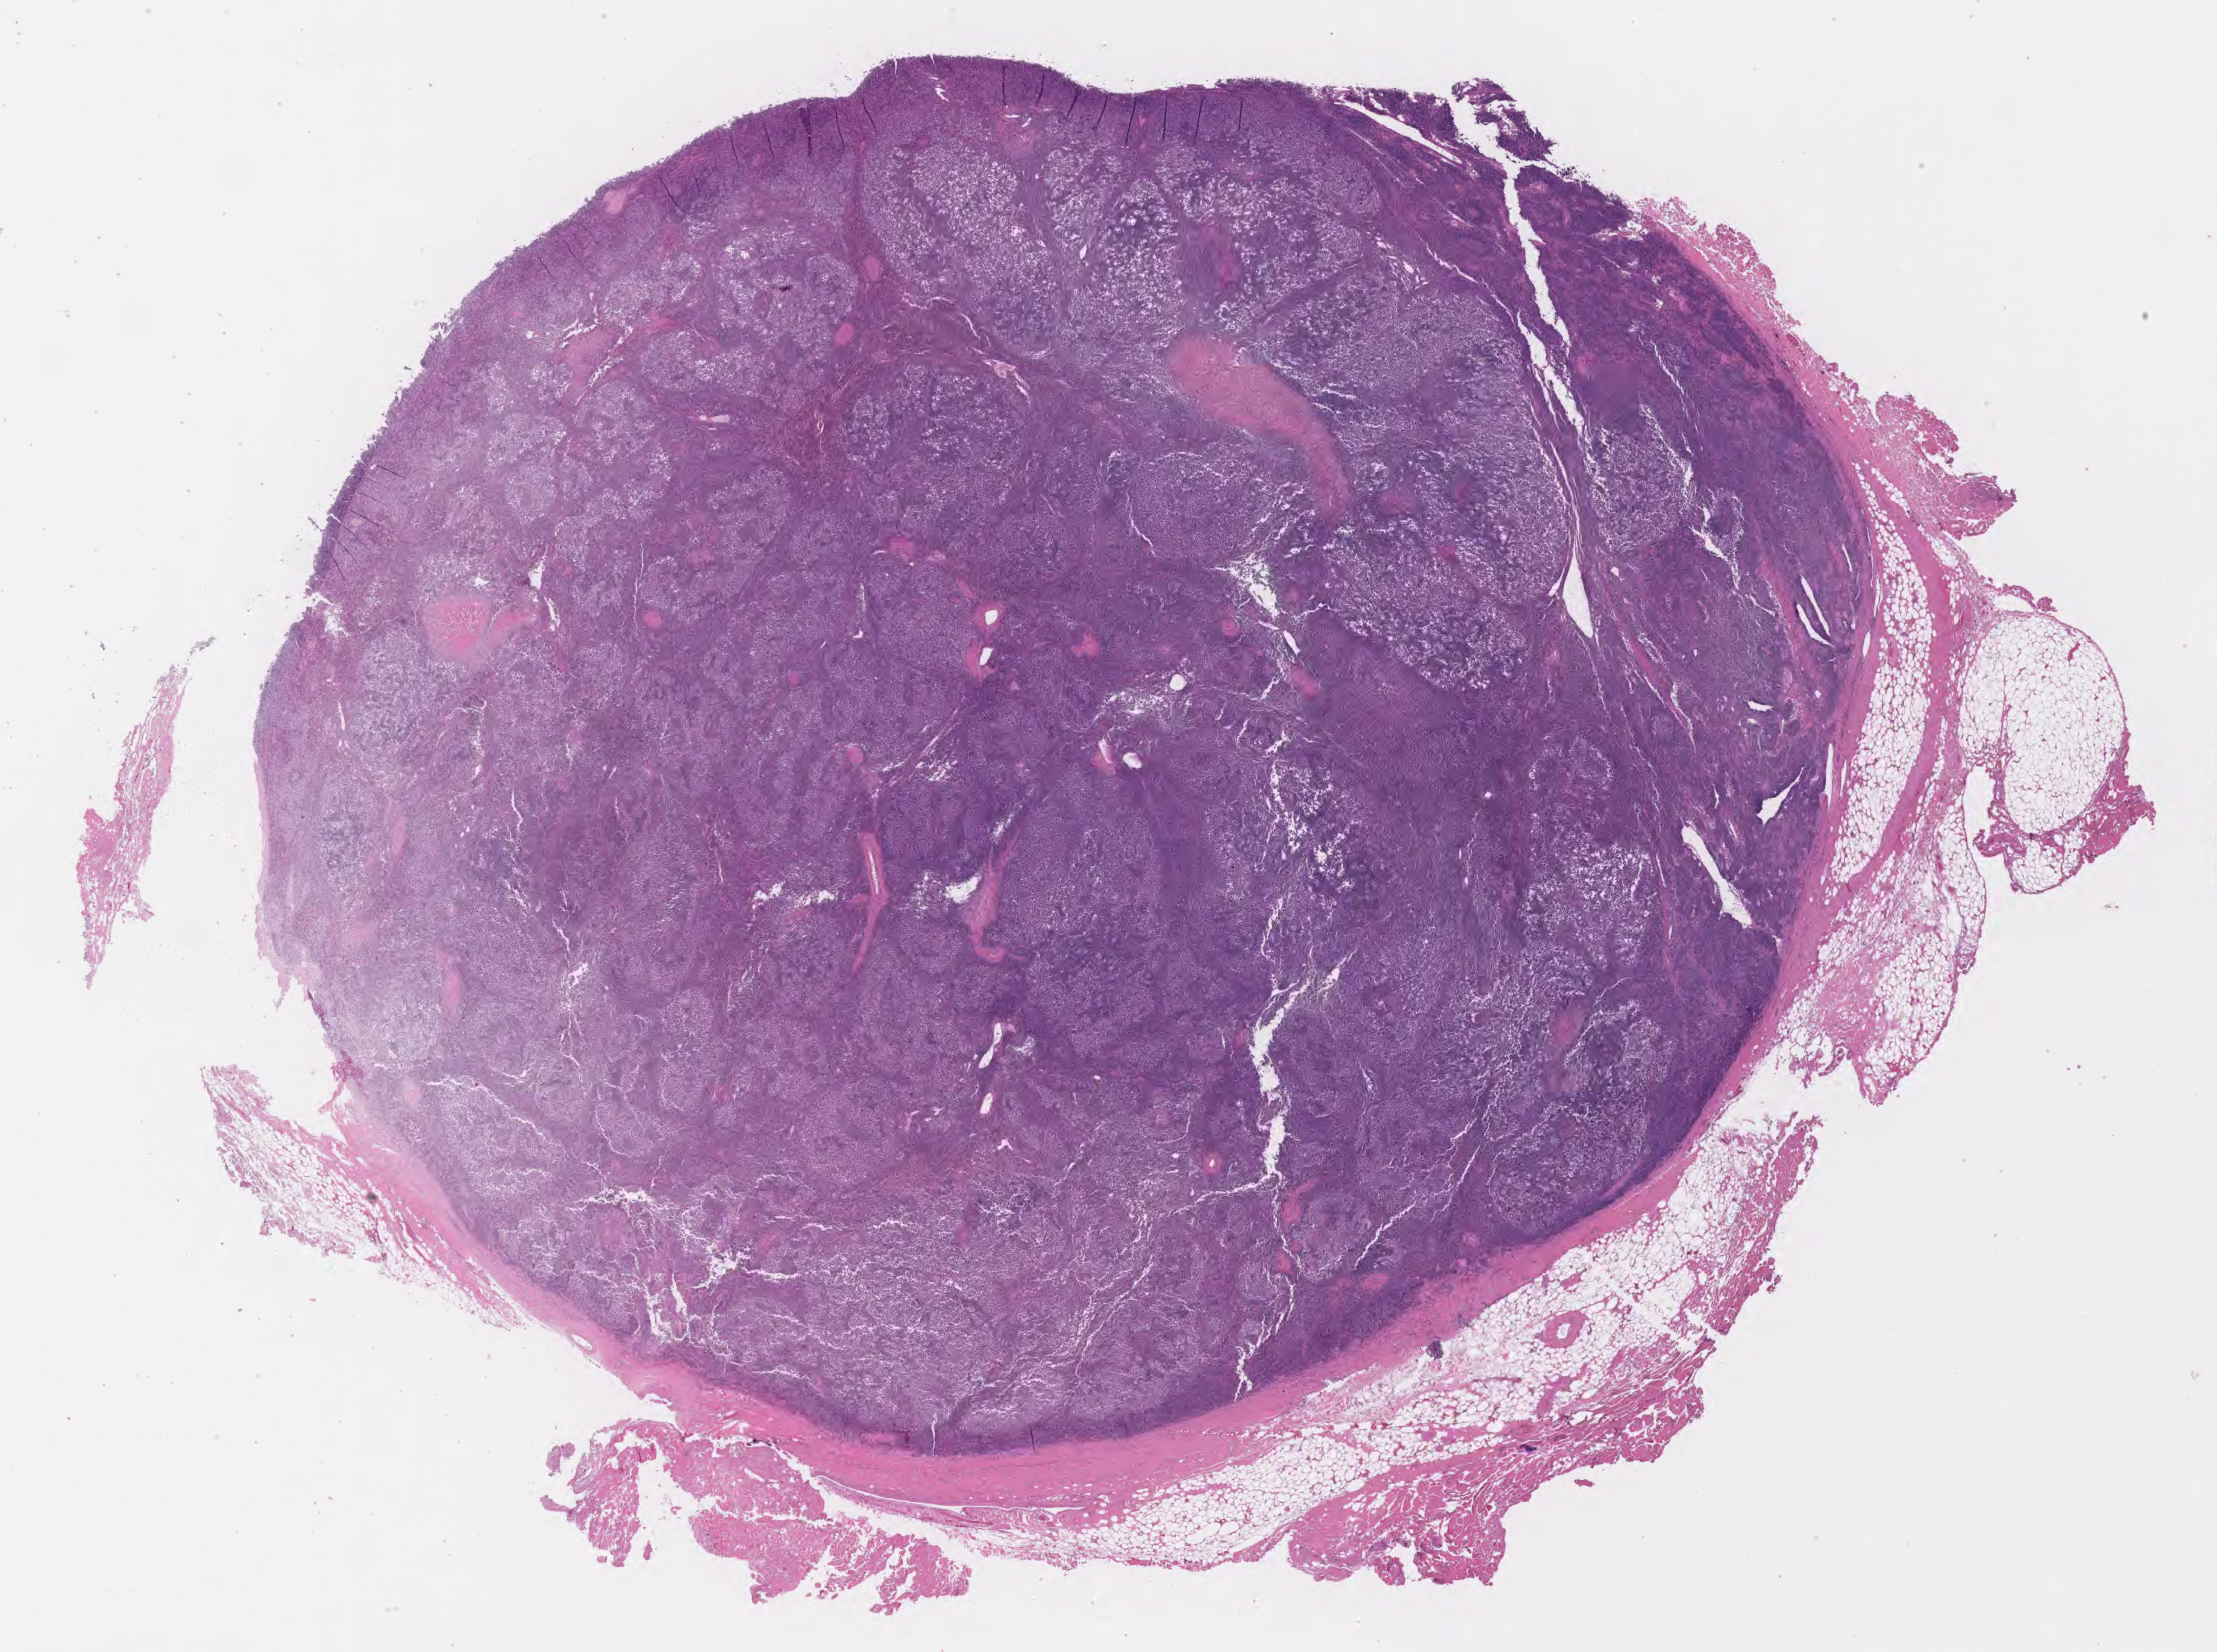
Hematoxylin and eosin (H&E) whole-slide image — a low-resolution overview of the entire scanned area, about 23.6 x 17.6 mm, specimen: tumor tissue, site: lymph node. Male patient, 46 years old.
- histologic diagnosis: Diffuse large B-cell lymphoma, NOS